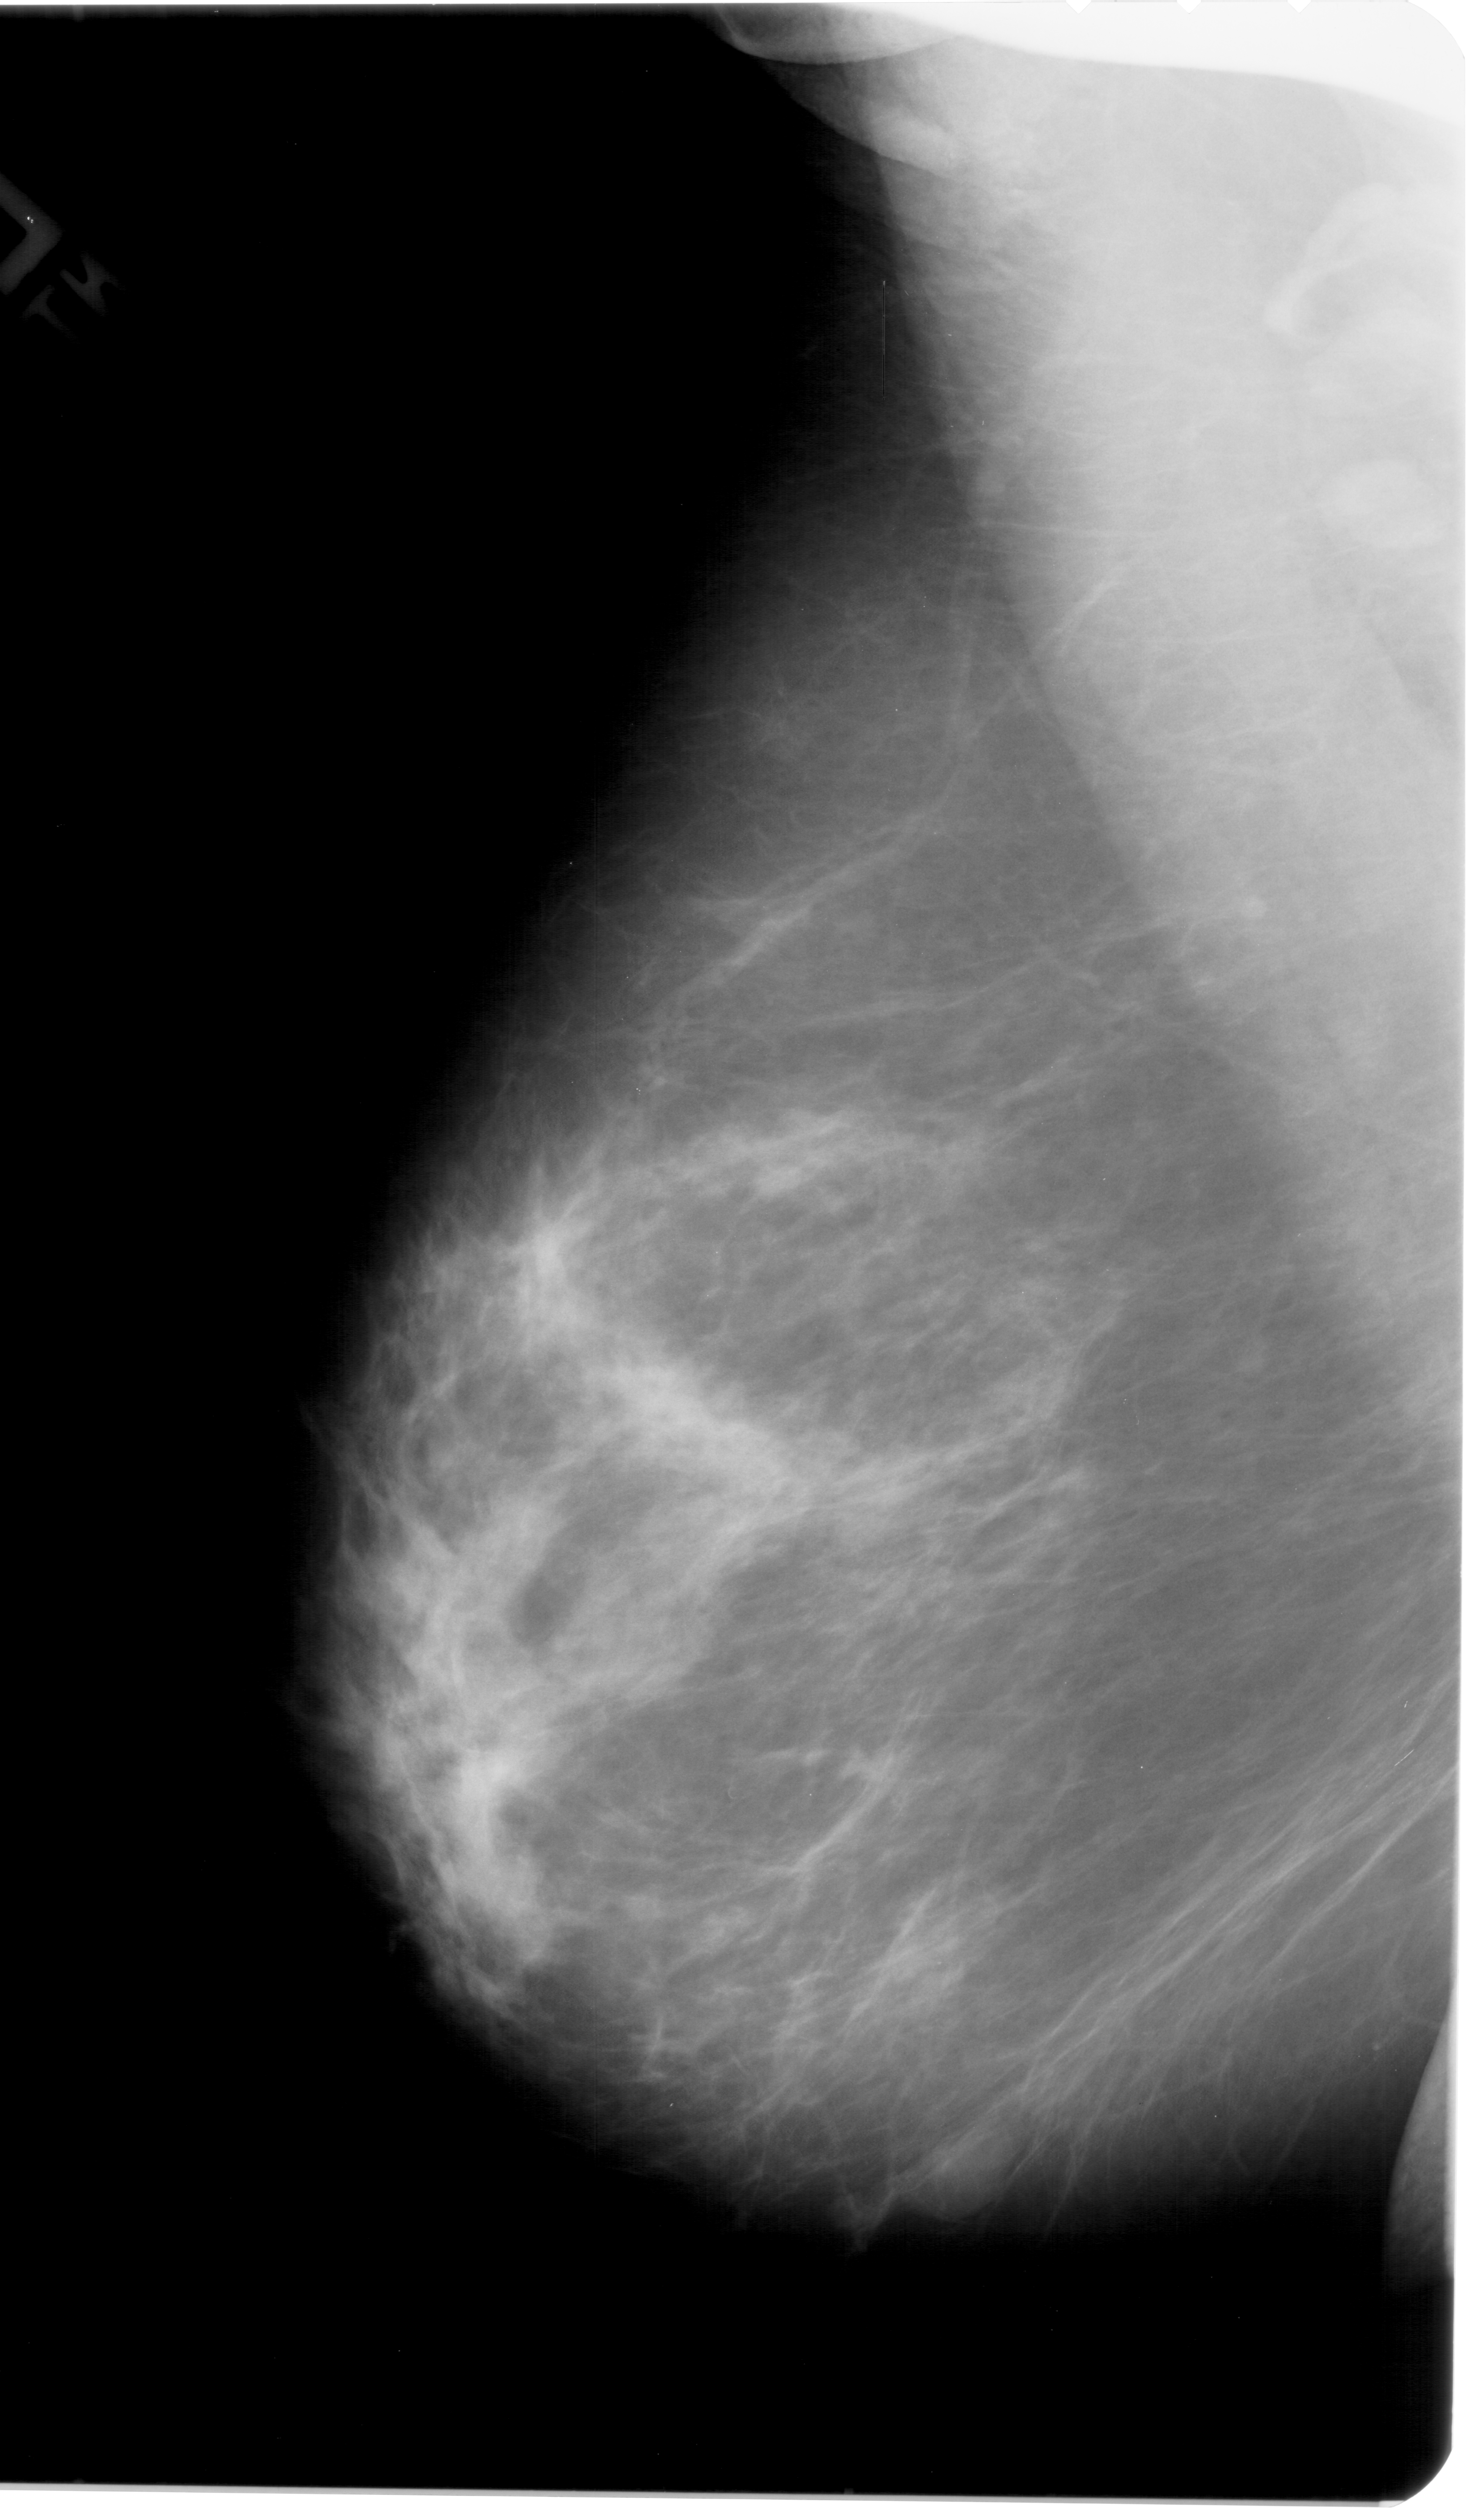
Mammogram (digitized film); left breast; MLO view; breast composition: heterogeneously dense (BI-RADS density category 3 of 4).
Radiologist-marked abnormalities on this image: mass, shape lobulated, margins obscured; BI-RADS assessment category 4; pathology result (as recorded, not read from the image): benign.